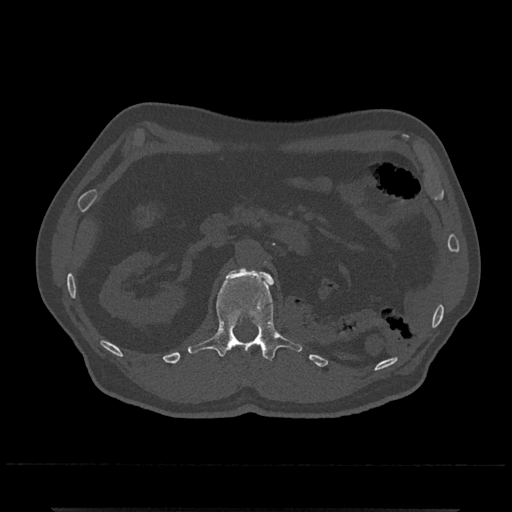
CT including the spine, one axial slice; position 365 of 797 along the scan axis; 120 kVp; bone window (W 1800 / L 400 HU); 0.5 mm slice thickness; 512 × 512 image matrix. Male patient, age 67 years. From the clinical record (not read from this slice): primary cancer: prostate.
Outlined on this slice (semi-automatically segmented with operator editing):
- L1 vertebra: box from (x=187, y=268) to (x=303, y=361) px